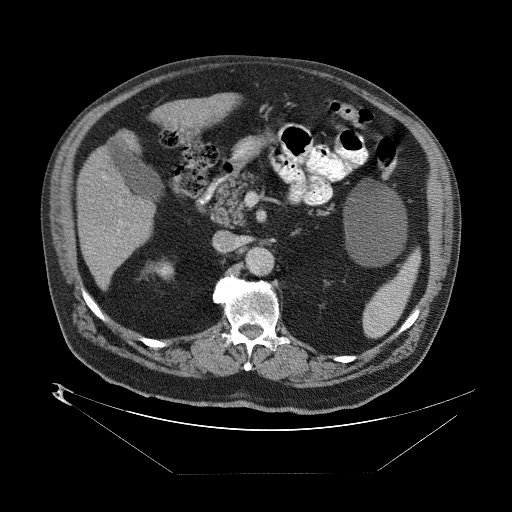
Contrast-enhanced abdominal CT (liver protocol), one axial slice. Position 31 of 89 along the scan axis. Reconstruction kernel STANDARD. 140 kVp. One of 2 acquisitions stored at this slice position. Soft-tissue window (W 400 / L 40 HU). 2.5 mm slice thickness. 512 × 512 image matrix. From the clinical record (not read from this slice): diagnosis: hepatocellular carcinoma (patient treated with transarterial chemoembolisation; whether this scan precedes or follows treatment is not stated here); TNM stage (as recorded): Stage-II; Child-Pugh class: B; tumour nodularity: multinodular.
Annotated regions visible in this slice (semi-automatically segmented with operator editing):
- abdominal aorta: box from (x=247, y=250) to (x=272, y=276) px
- liver parenchyma outside the tumour (the mass and vessels are separate outlines, so this box may not span the whole liver): (x=76, y=94)–(x=232, y=290)
- liver vessels: (x=88, y=182)–(x=133, y=256)